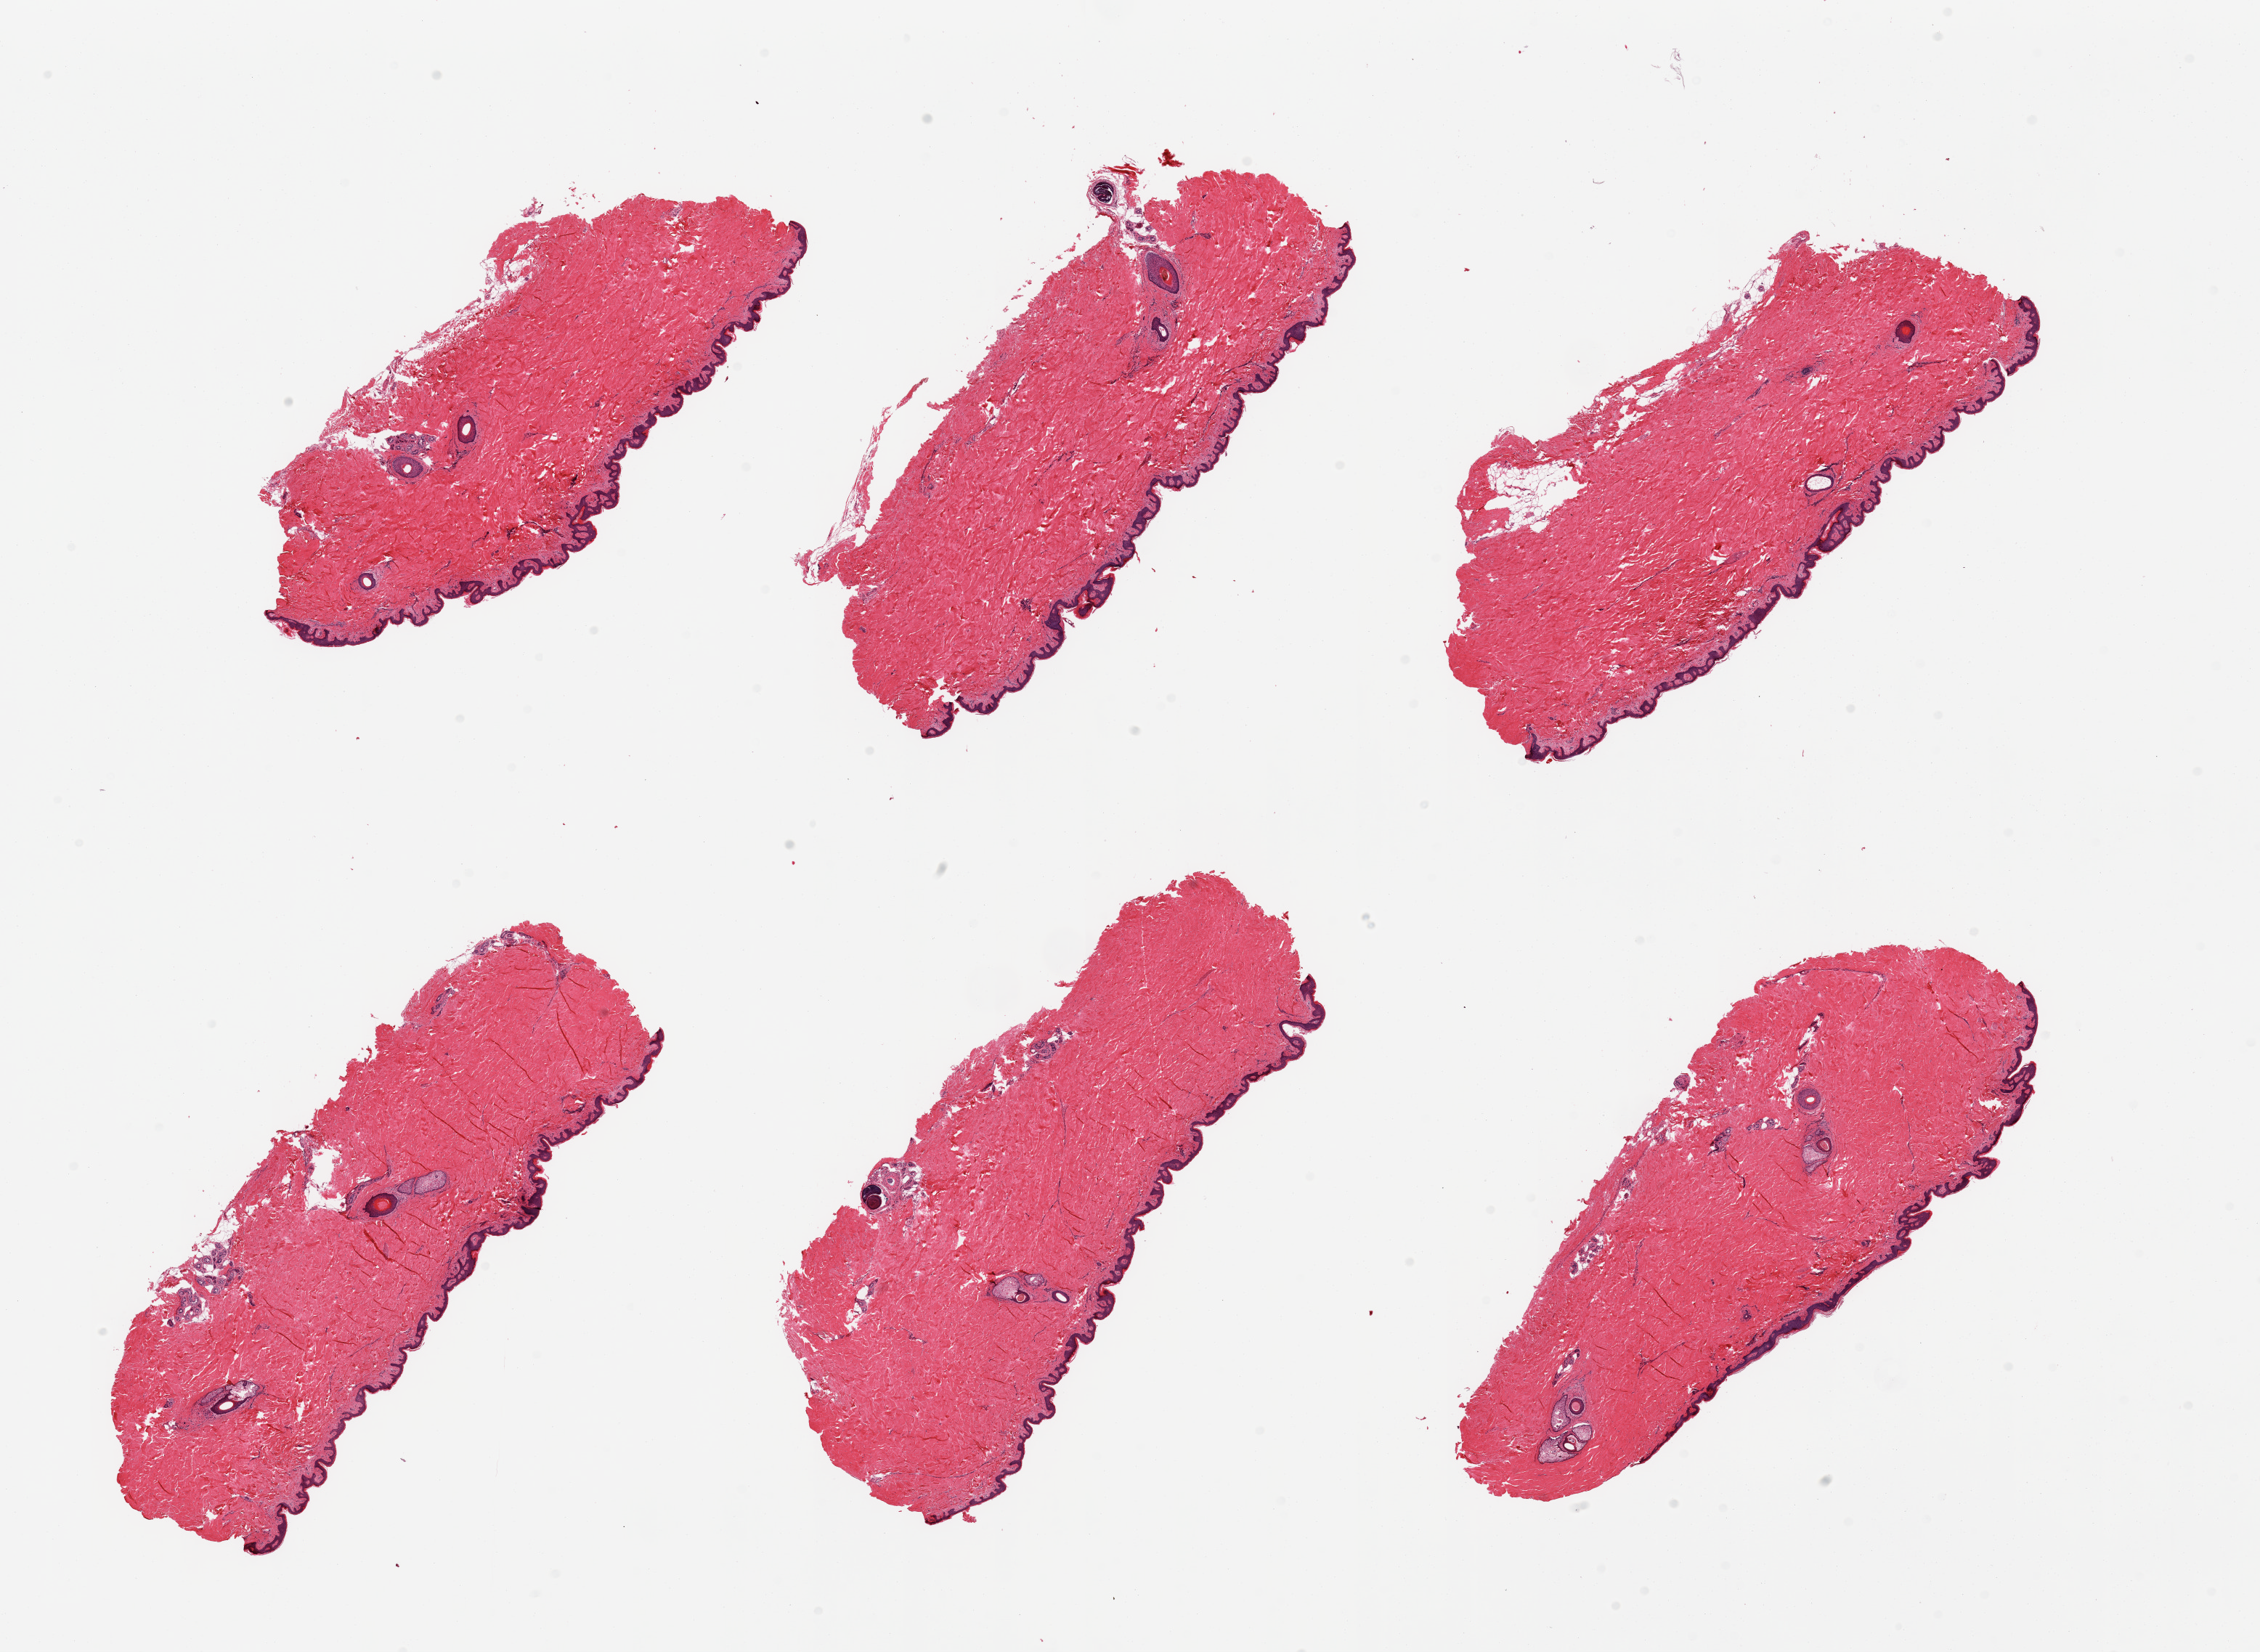
Haematoxylin and eosin whole-slide image — whole scanned area (about 24.6 x 18.0 mm, from a 20x scan) shown as a low-resolution overview, PAXgene-fixed, paraffin-embedded tissue, sampled site (target tissue): skin of suprapubic region, tissue donor sample. Donor: male.
Pathologist's review note for this sample: 6 pieces; well trimmed; 5% dermal fat.